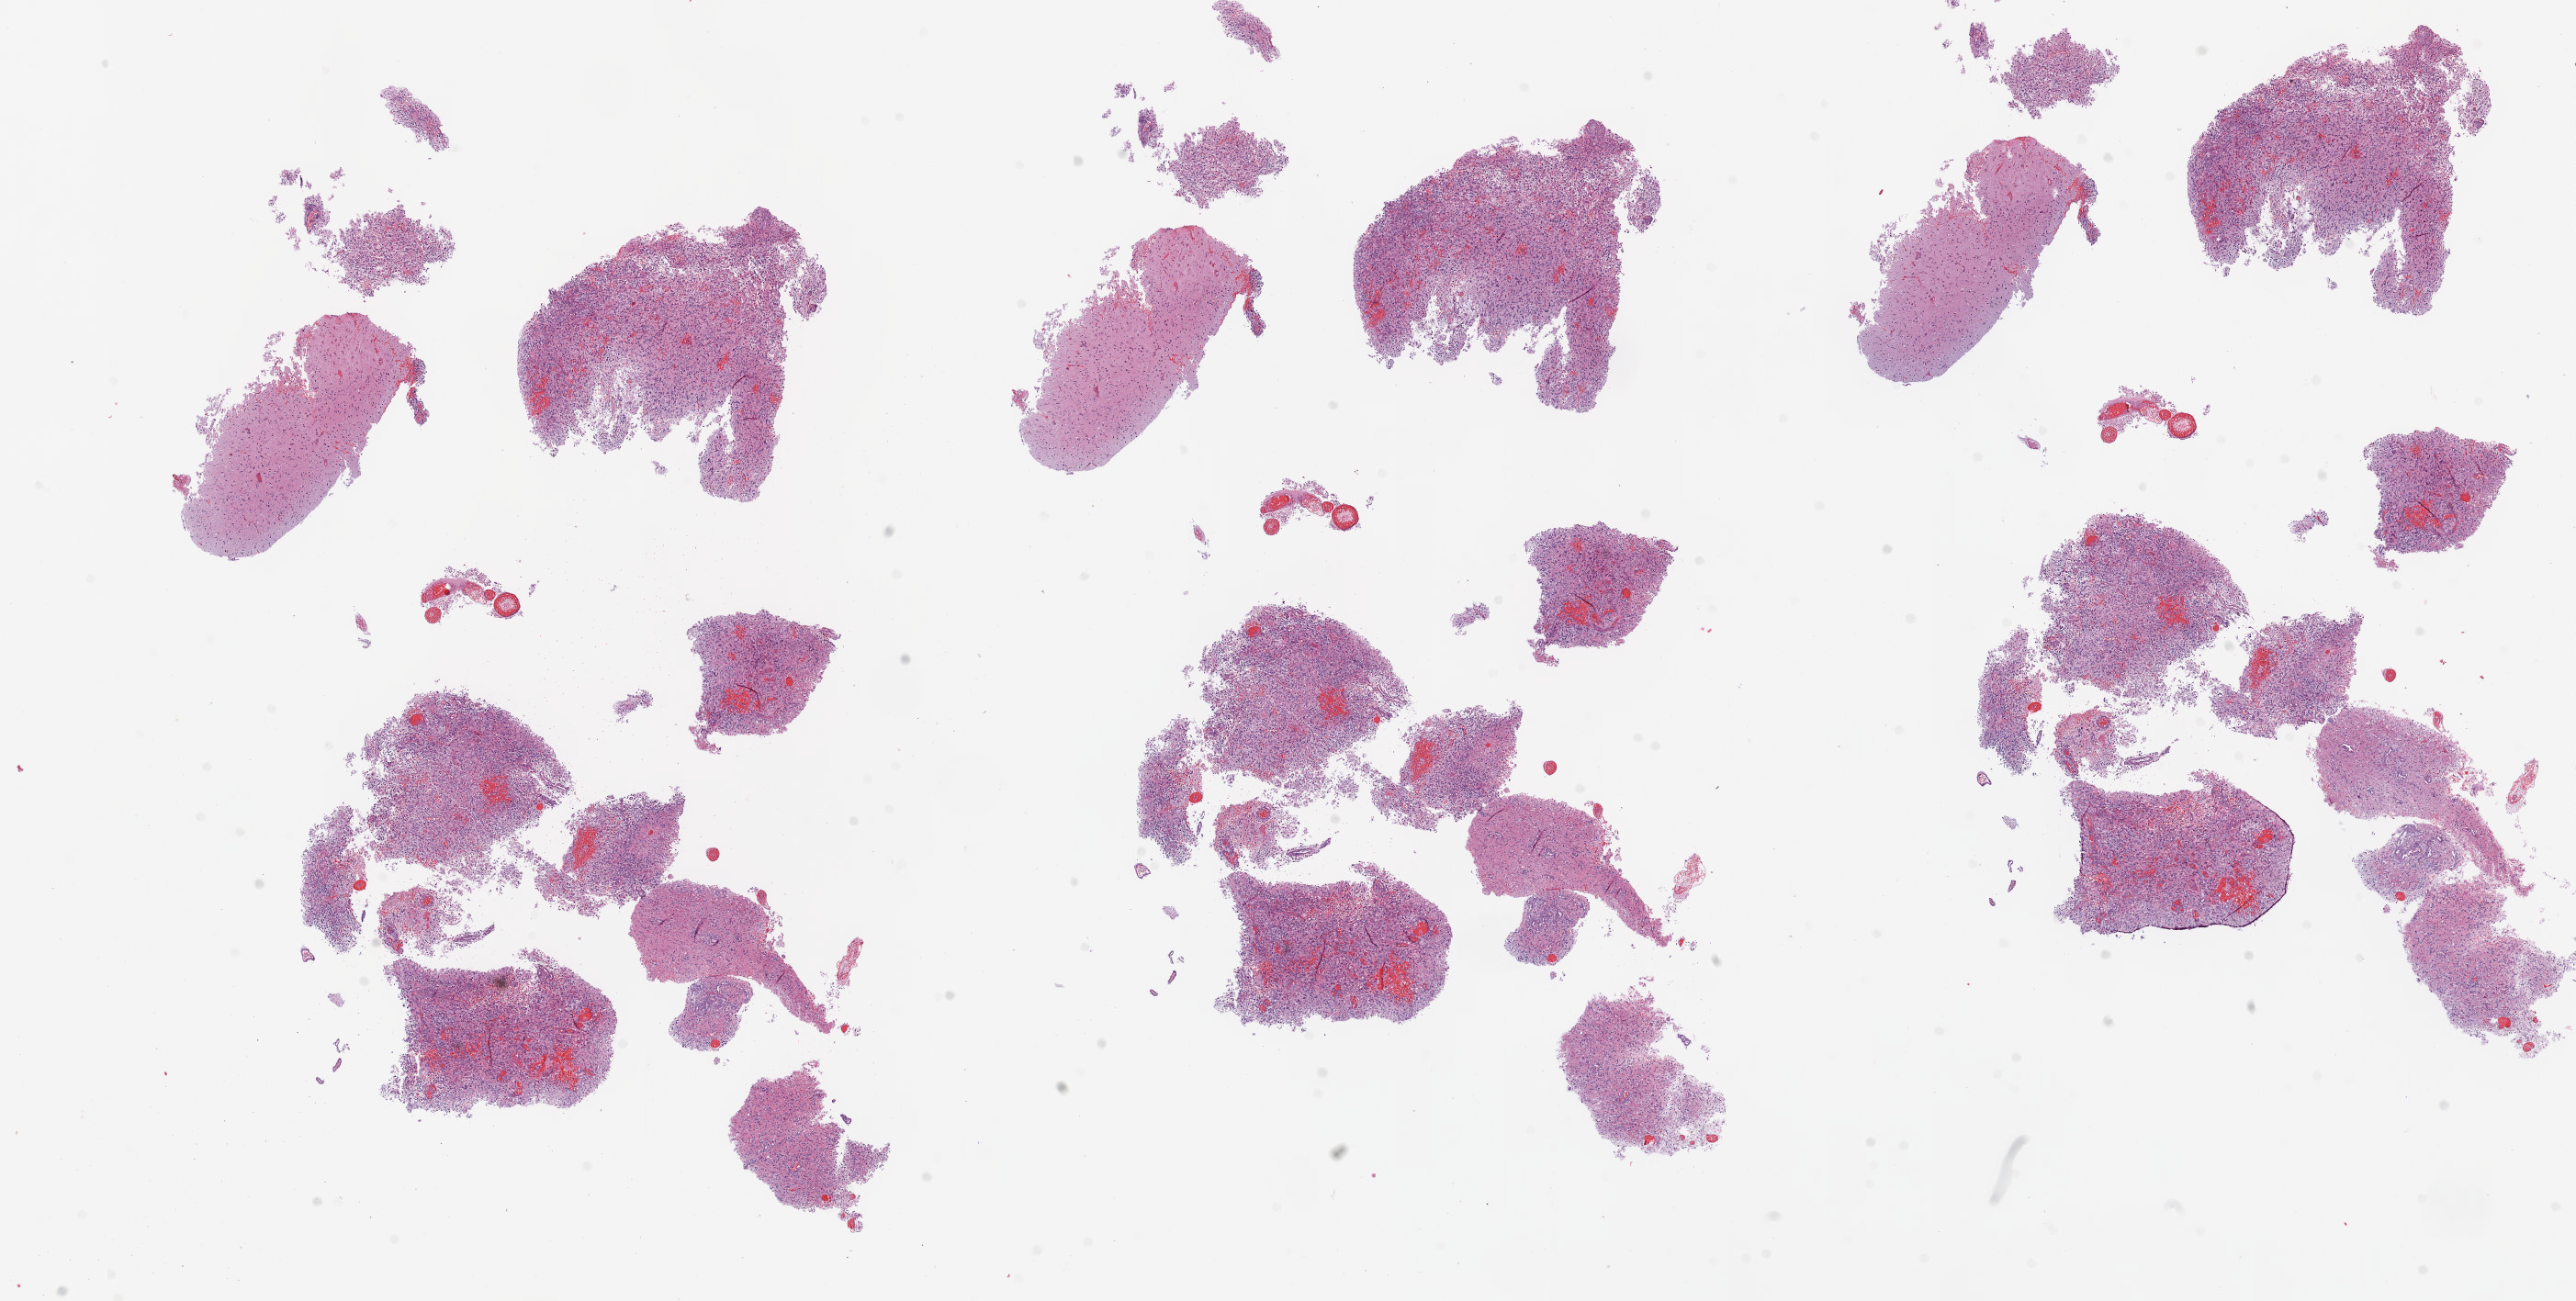
Whole-slide histology image, H&E-stained — whole scanned area (about 22.5 x 11.4 mm, slide scanned at 5x) shown as a low-resolution overview, frozen section from the top of the tissue portion, brain, primary tumour sample. Male, age 51 years at initial diagnosis. Composition of this section per pathologist review: tumour cells 100%, tumour nuclei 80%.
Pathologic diagnosis: Glioblastoma.